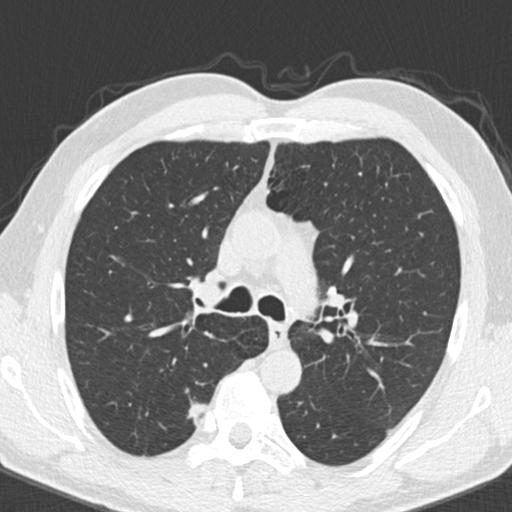
Low-dose screening chest CT, one axial slice. Slice 131 of 192 in the series (ordered by position). Reconstruction kernel B30f. 120 kVp. Lung window (W 1500 / L -600 HU). 512 × 512 image matrix, field of view 307 × 307 mm.
Structures marked on this image (outlined manually by an expert reader):
- lesion 1 (tumor, upper lobe of right lung): bounding box <187,402,207,425> (left, top, right, bottom; pixels)